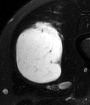
MRI of an extremity soft-tissue mass, one axial slice. Slice 27 of 65 in the series (ordered by position). T2-weighted fat-saturated. MR volume resampled by the dataset authors to the PET/CT grid (not the native acquisition matrix). 90 × 105 image matrix, field of view 88 × 103 mm. Male patient. Case-level facts recorded for this patient, not image findings: histological type: mixoid liposarcoma; grade: low; site of the primary tumour: left thigh.
Annotated regions visible in this slice (expert contour drawn on MRI and transferred to this co-registered scan by the dataset authors):
- gross tumour volume (mass): bounding box [x1, y1, x2, y2] px = [14, 21, 62, 83]